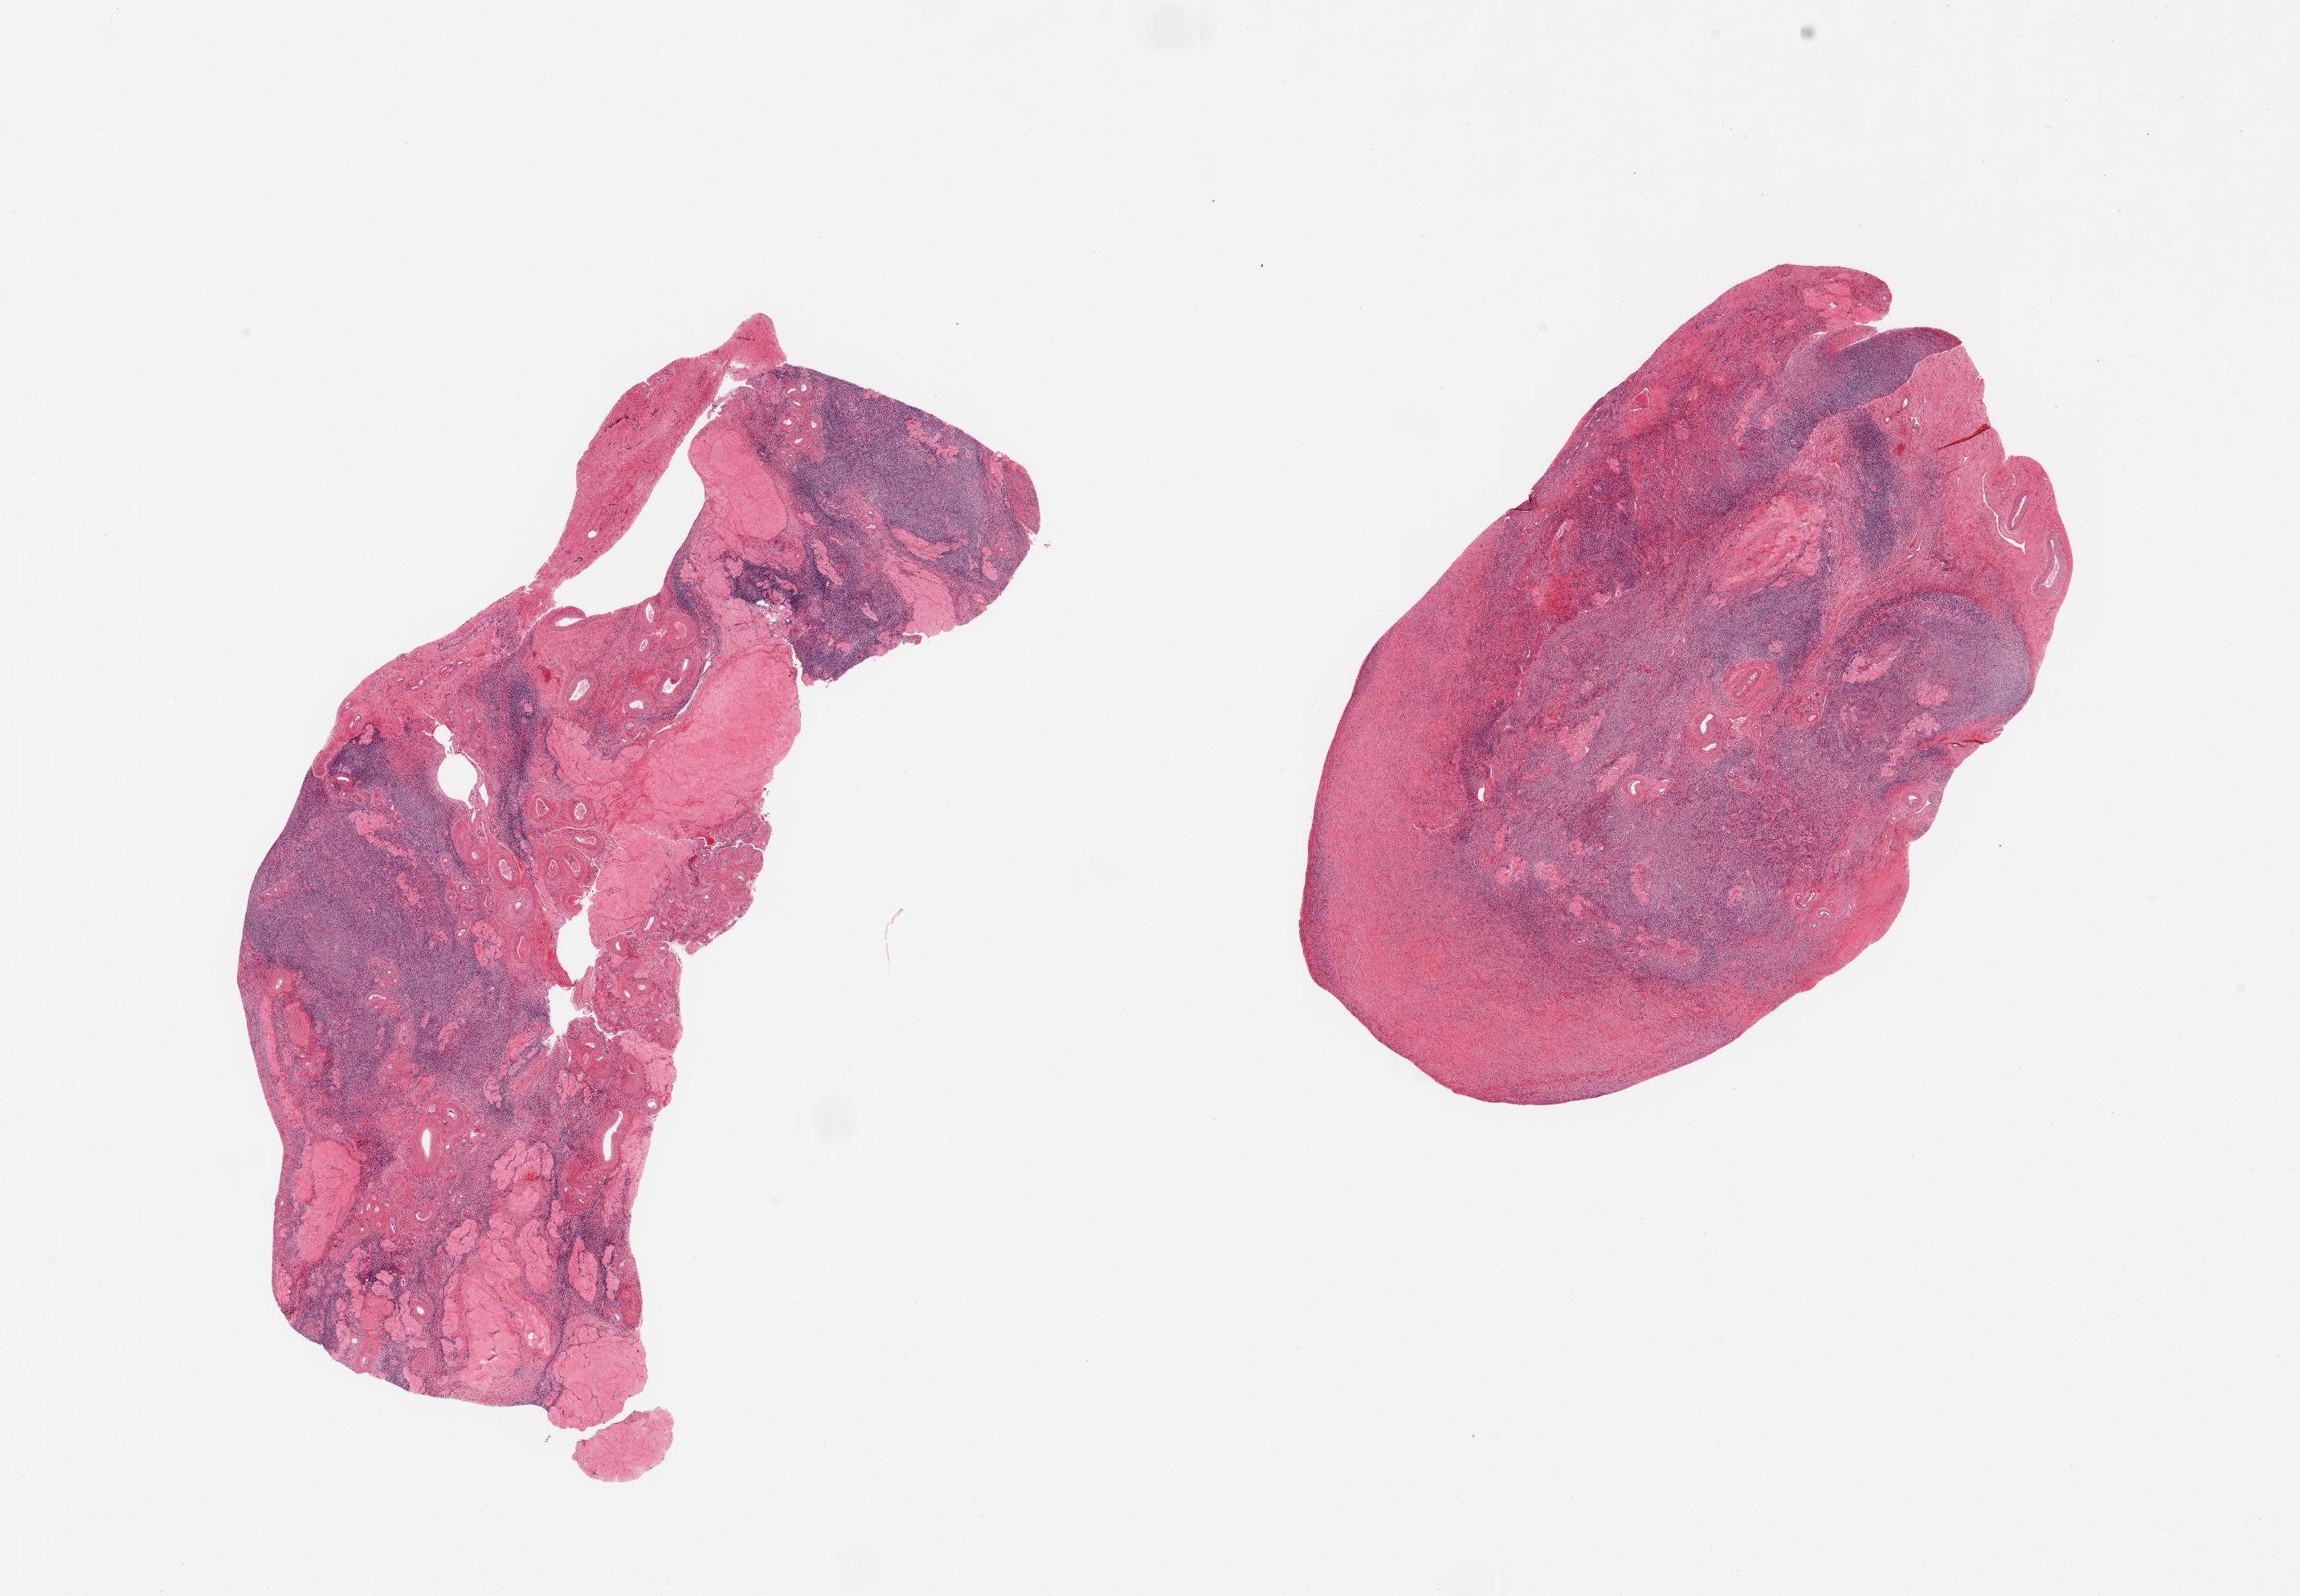
Hematoxylin and eosin (H&E) whole-slide image, shown as a low-resolution overview of the whole scanned area (about 22.6 x 15.7 mm). PAXgene-fixed paraffin-embedded (PFPE) section. Sampled site (target tissue): ovary. Donor tissue sample.
Reviewer comment on this tissue sample: 2 pieces; atrophic with numerous corpora albicantia.